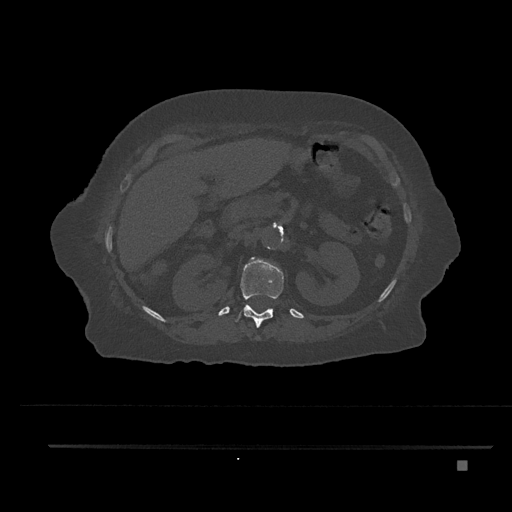
CT including the spine, one axial slice; slice 257 of 797 in the series (ordered by position); reconstruction kernel Br40s/3; bone window (W 1800 / L 400 HU); 512 × 512 image matrix, field of view 437 × 437 mm. Female patient, age 76 years. Case-level facts recorded for this patient, not image findings: primary cancer: lung.
Annotated regions visible in this slice (semi-automatically segmented with operator editing):
- L1 vertebra: bounding box <250,258,259,261> (left, top, right, bottom; pixels)
- T12 vertebra: <235,259,283,328>